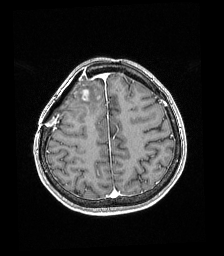
Brain MRI from a brain-tumour surgery series, one axial slice. Position 57 of 192 along the scan axis. T1-weighted post-contrast. 1 mm slice thickness. 224 × 256 image matrix. From the clinical record (not read from this slice): histopathology: Astrocytoma; WHO grade: 4; IDH mutation: yes; tumour location: Right superficial frontal.
Outlined on this slice (expert manual segmentation):
- tumour: bounding box <78,89,89,101> (left, top, right, bottom; pixels)